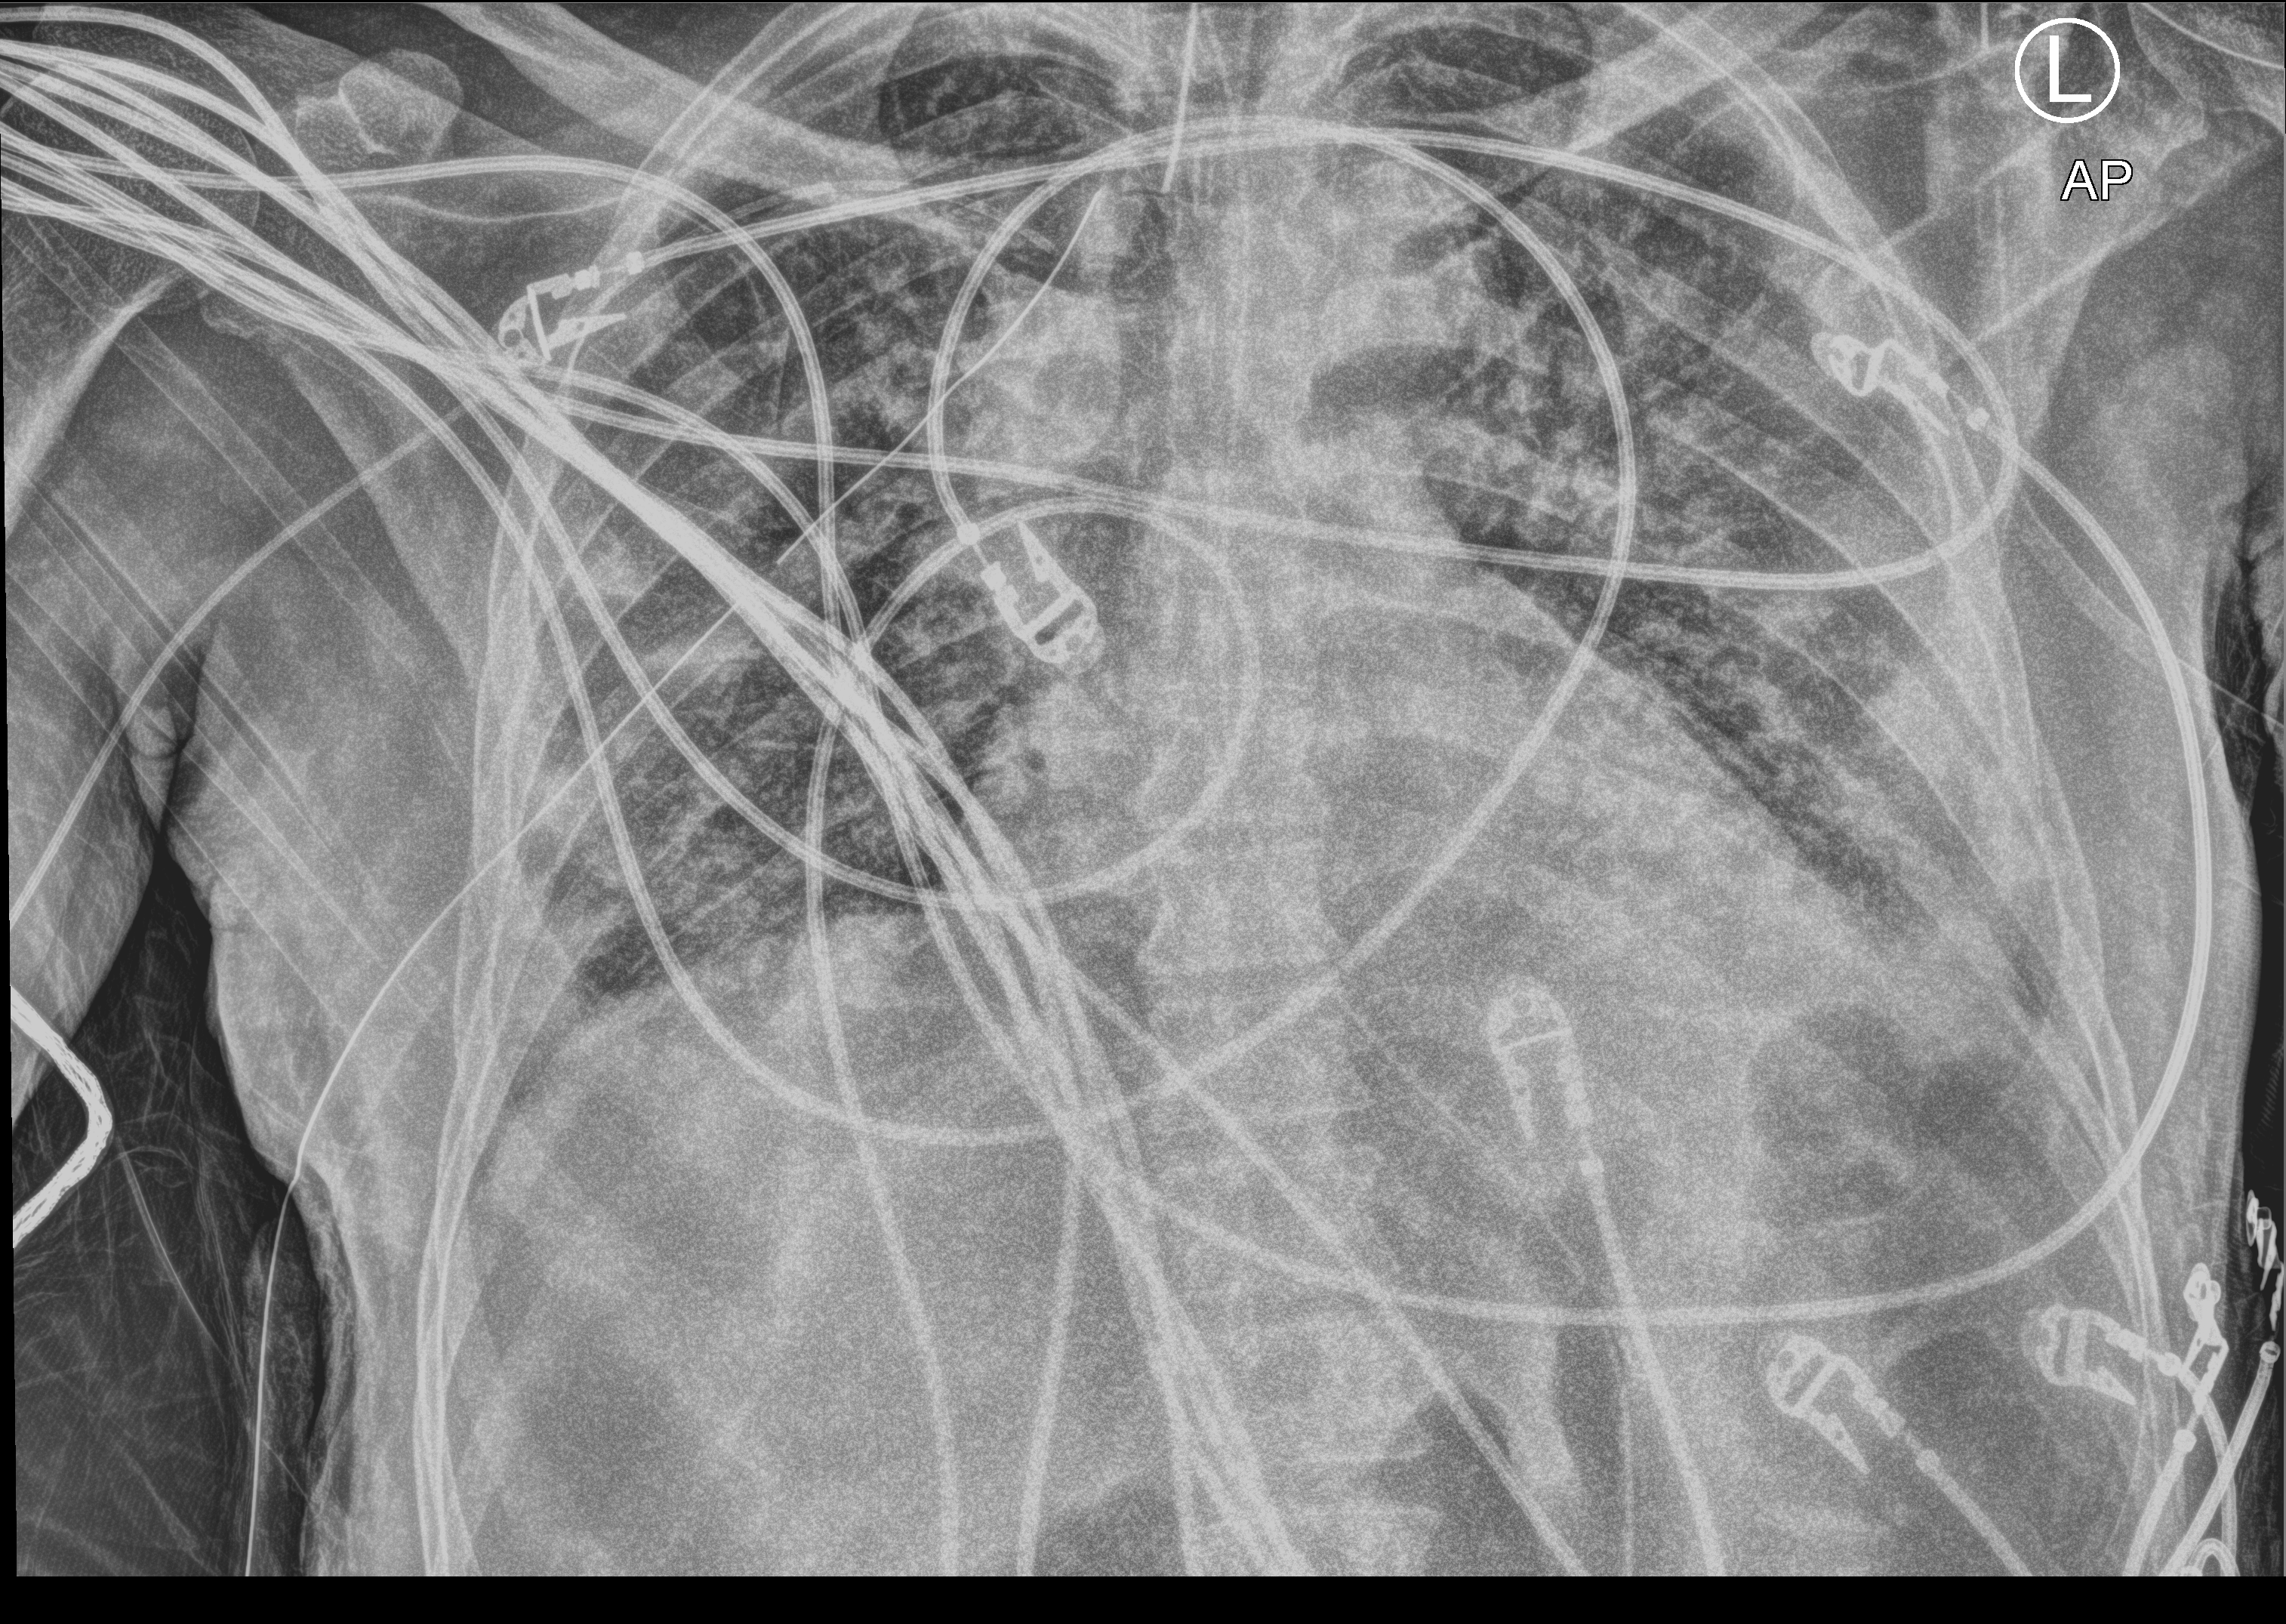
Chest X-ray (portable); anteroposterior (AP) projection. Patient hospitalised with COVID-19; male, aged 18–59 years.
From the hospital-stay record, not from the radiograph (when in the stay this image was taken is not recorded): mechanically ventilated during this hospital stay: yes; admitted to intensive care during this hospital stay: yes.